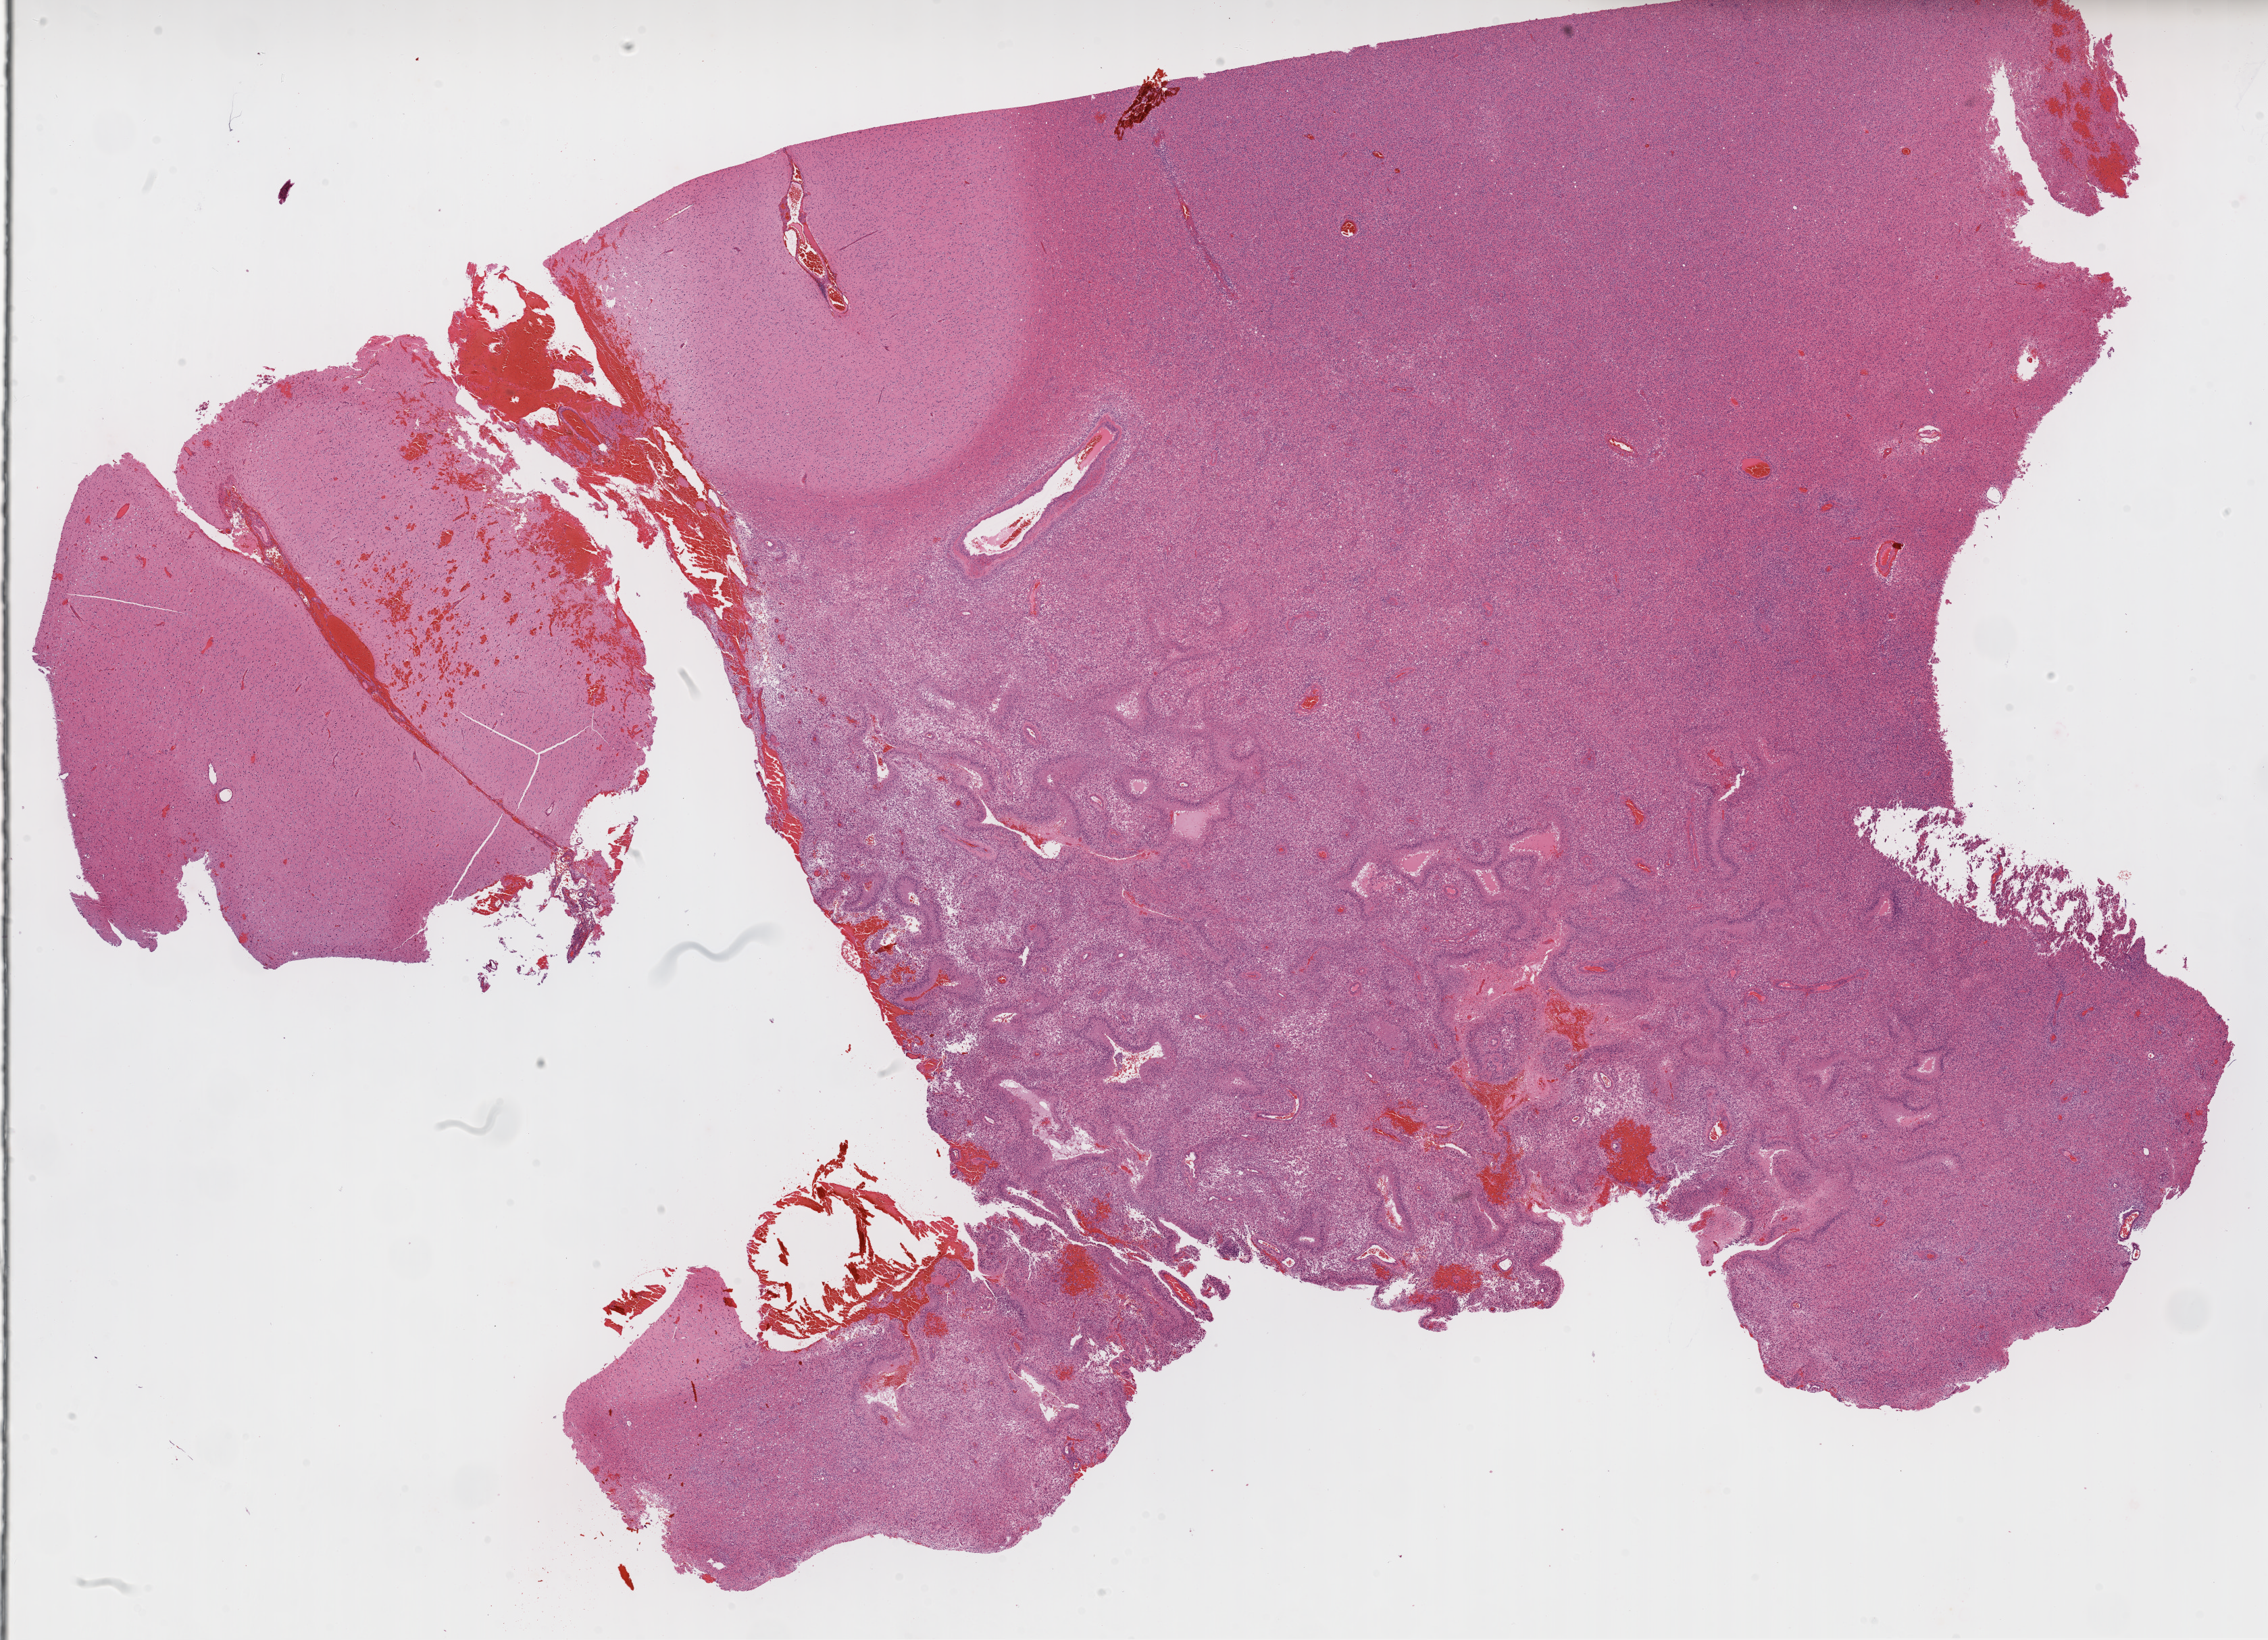
Digitized H&E tissue section (whole slide) — whole scanned area (about 27.1 x 19.6 mm, from a 20x scan) shown as a low-resolution overview; formalin-fixed paraffin-embedded (FFPE) diagnostic section; brain, primary tumour sample. Male, age 66 years at initial diagnosis.
Diagnosis: Glioblastoma.